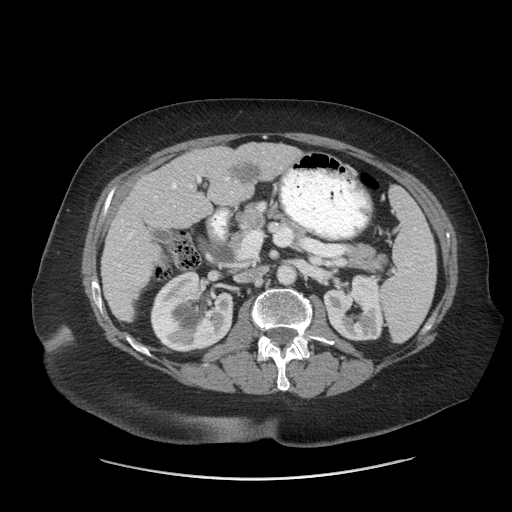
Contrast-enhanced abdominal CT (liver protocol), one axial slice; position 26 of 69 along the scan axis; soft-tissue window (W 400 / L 40 HU); 2.5 mm slice thickness; 512 × 512 image matrix, field of view 420 × 420 mm. Case-level facts recorded for this patient, not image findings: diagnosis: hepatocellular carcinoma (patient treated with transarterial chemoembolisation; whether this scan precedes or follows treatment is not stated here); TNM stage (as recorded): Stage-IIIB; Child-Pugh class: A.
Structures marked on this image (semi-automatic segmentation, software-assisted and operator-edited):
- liver parenchyma outside the tumour (the mass and vessels are separate outlines, so this box may not span the whole liver): bounding box [x1, y1, x2, y2] px = [100, 142, 301, 321]
- liver vessels: [114, 175, 229, 267]